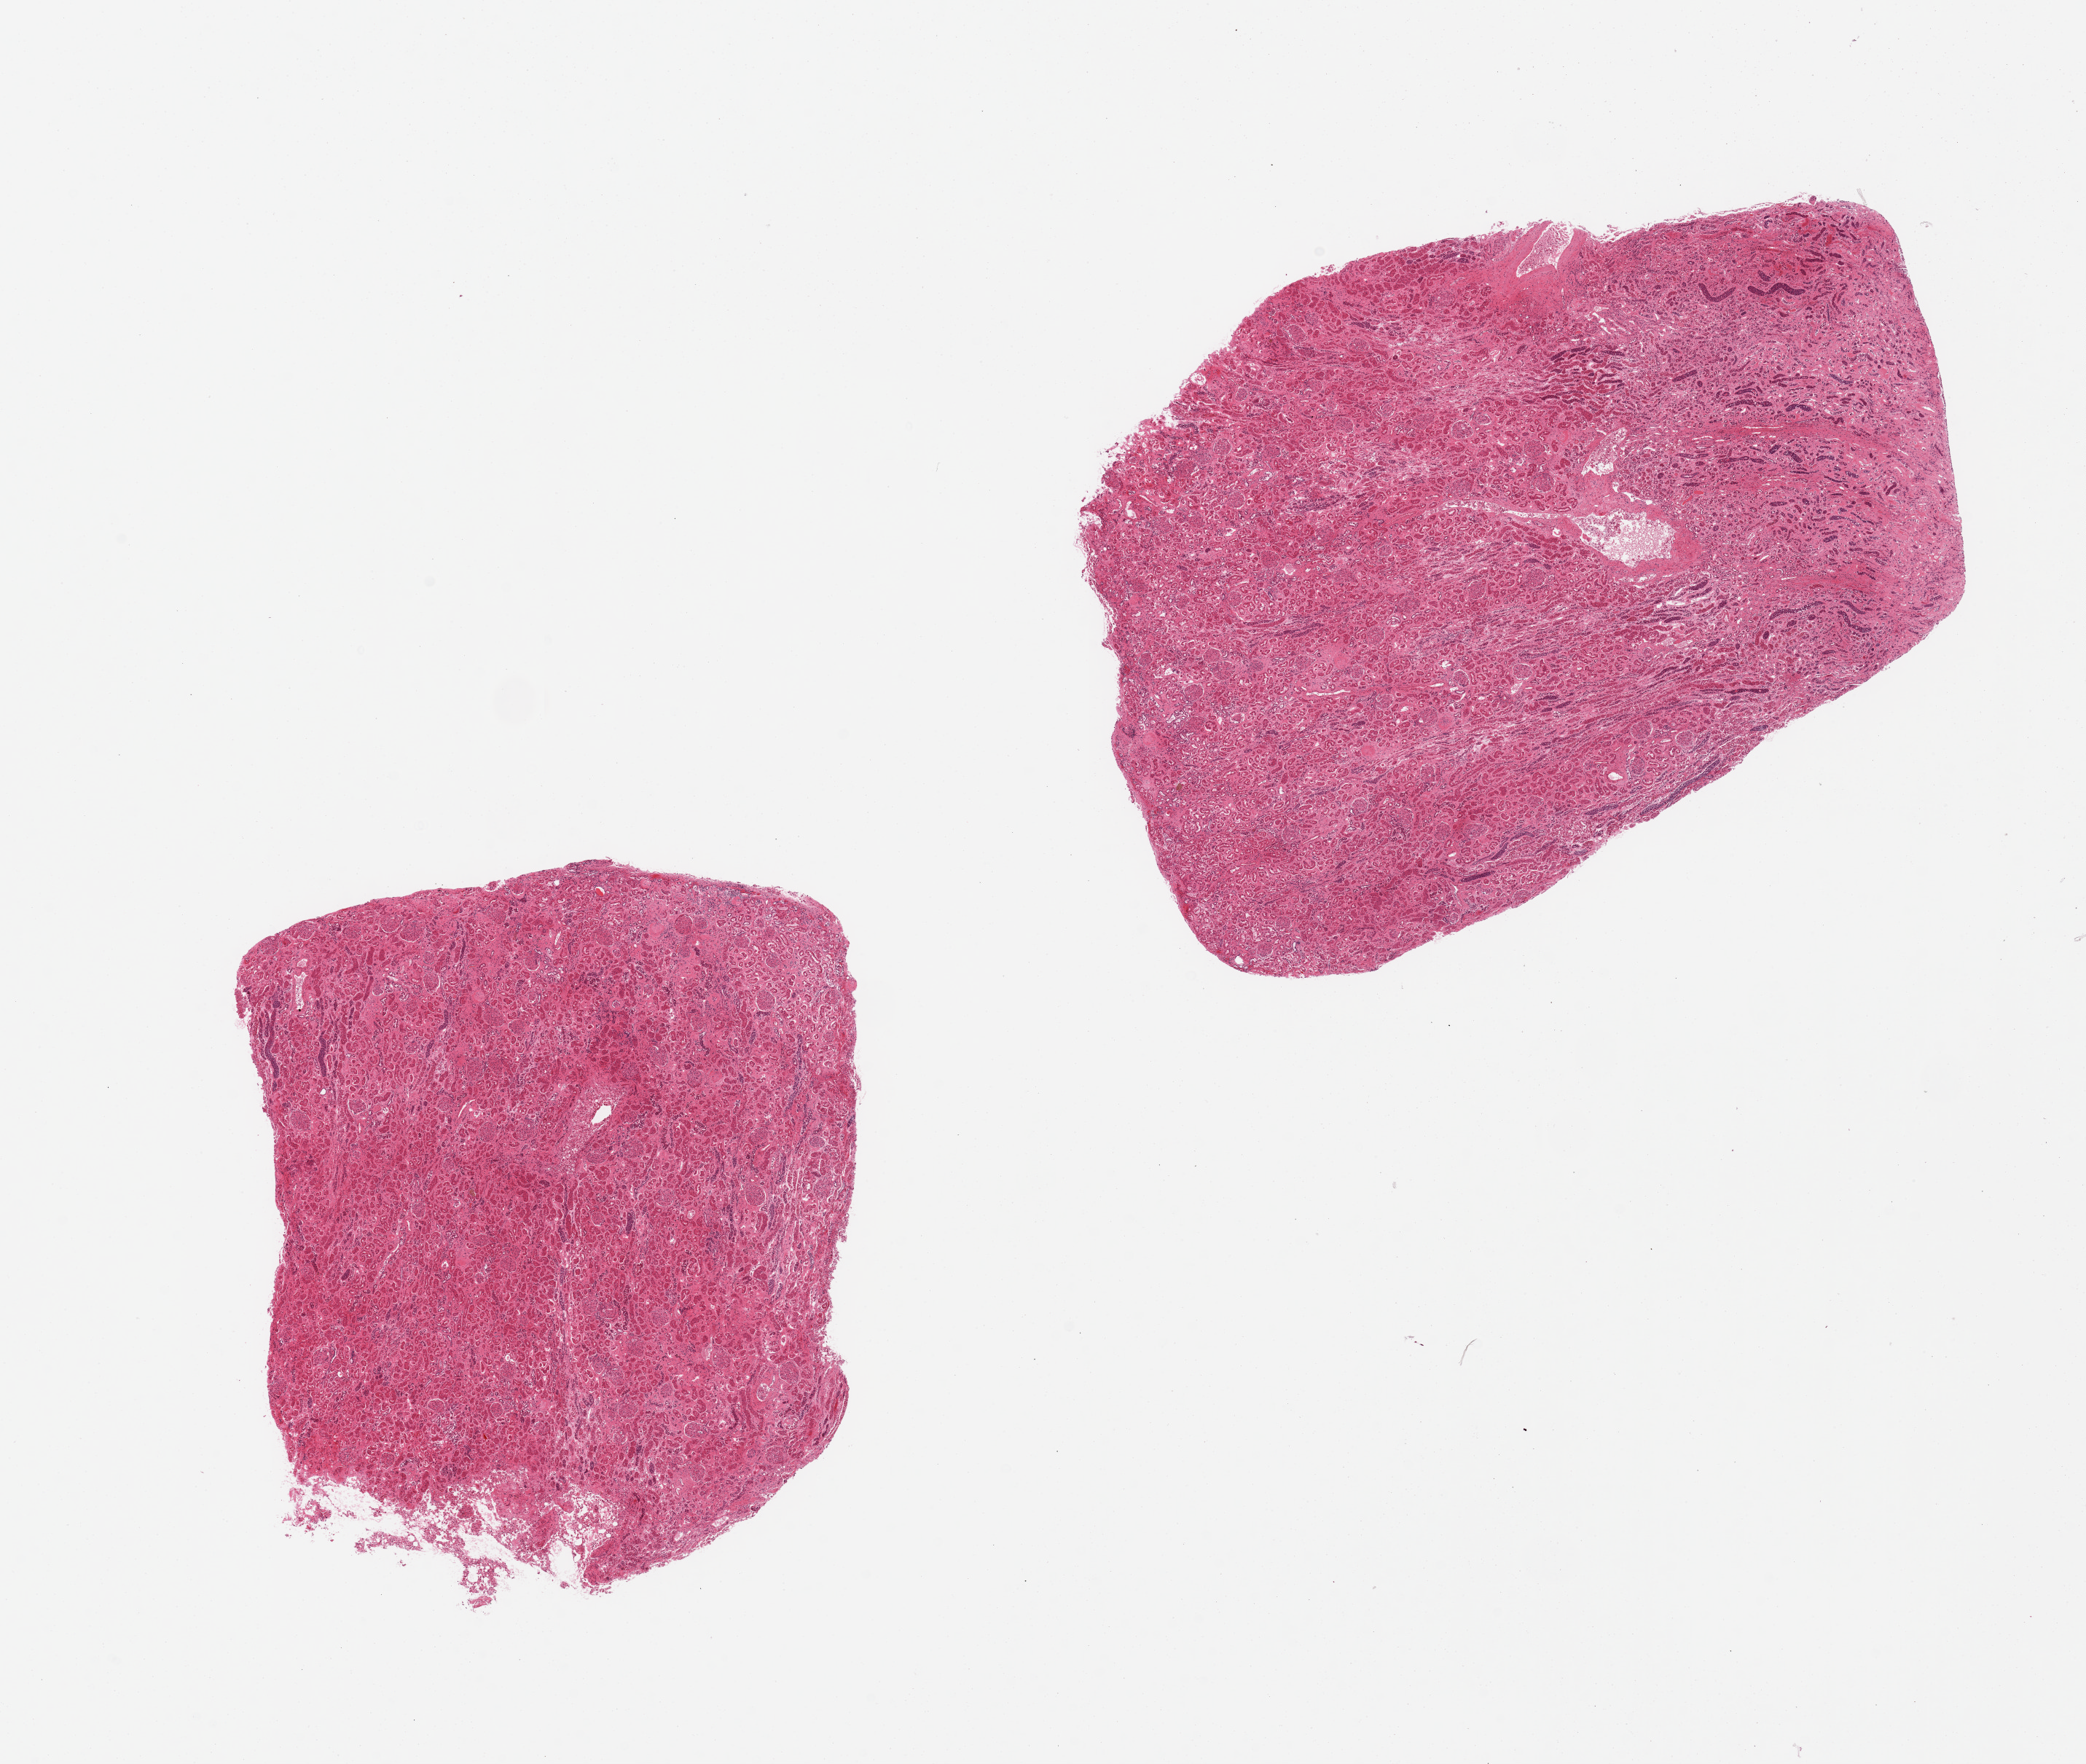
Whole-slide image, haematoxylin and eosin stain, shown as a low-resolution overview of the whole scanned area (about 22.6 x 19.1 mm, acquisition: 20x scan). PAXgene-fixed, paraffin-embedded tissue. Target tissue: renal cortex. Donor tissue sample. Donor: female.
- review note (as recorded): 2 pieces, glomeruli present in both